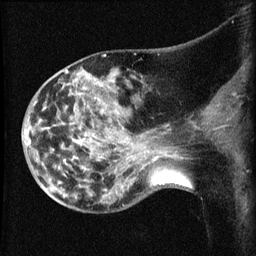
Breast MRI (dynamic contrast-enhanced), one sagittal slice; position 26 of 60 along the scan axis; dynamic contrast-enhanced series, image 2 of 3 at this slice position (ordered by acquisition); 1.5 T; TE 4.2 ms, TR 8.2 ms; 256 × 256 image matrix. Patient: female, 50 years.
Outlined on this slice (semi-automatic segmentation, software-assisted and operator-edited):
- analysis volume of interest (the breast-tissue region the enhancement analysis was run in; not a lesion): bounding box (x1, y1, x2, y2) in pixels: (38, 71, 169, 211)
- tumour enhancement mask (voxels above the 70 % enhancement threshold inside the analysis volume of interest): (66, 71, 157, 161)